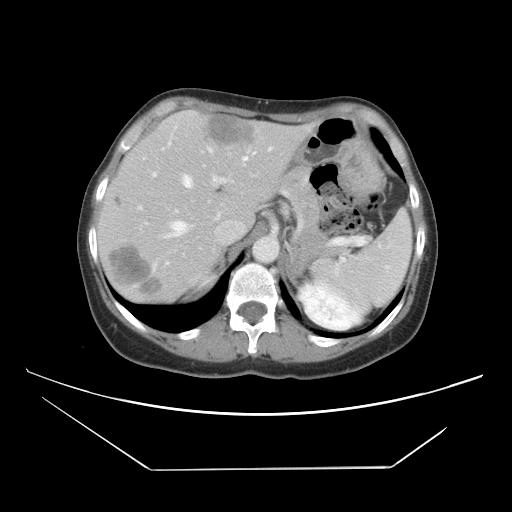
Contrast-enhanced abdominal CT, one axial slice. Position 31 of 42 along the scan axis. Soft-tissue window (W 400 / L 40 HU). 5 mm slice thickness. 512 × 512 image matrix, field of view 399 × 399 mm. Female patient, age 52 years. Case-level facts recorded for this patient, not image findings: diagnosis: colorectal cancer liver metastases, imaged before liver resection.
Annotated regions visible in this slice (expert manual segmentation):
- hepatic veins: bounding box <145,147,272,239> (left, top, right, bottom; pixels)
- liver: <99,113,308,301>
- planned liver remnant (the part of the liver to remain after resection): <117,119,239,226>
- portal vein (with intrahepatic branches): <137,148,288,213>
- liver metastasis: <210,119,255,145>
- liver metastasis: <115,197,124,207>
- liver metastasis: <111,248,162,297>